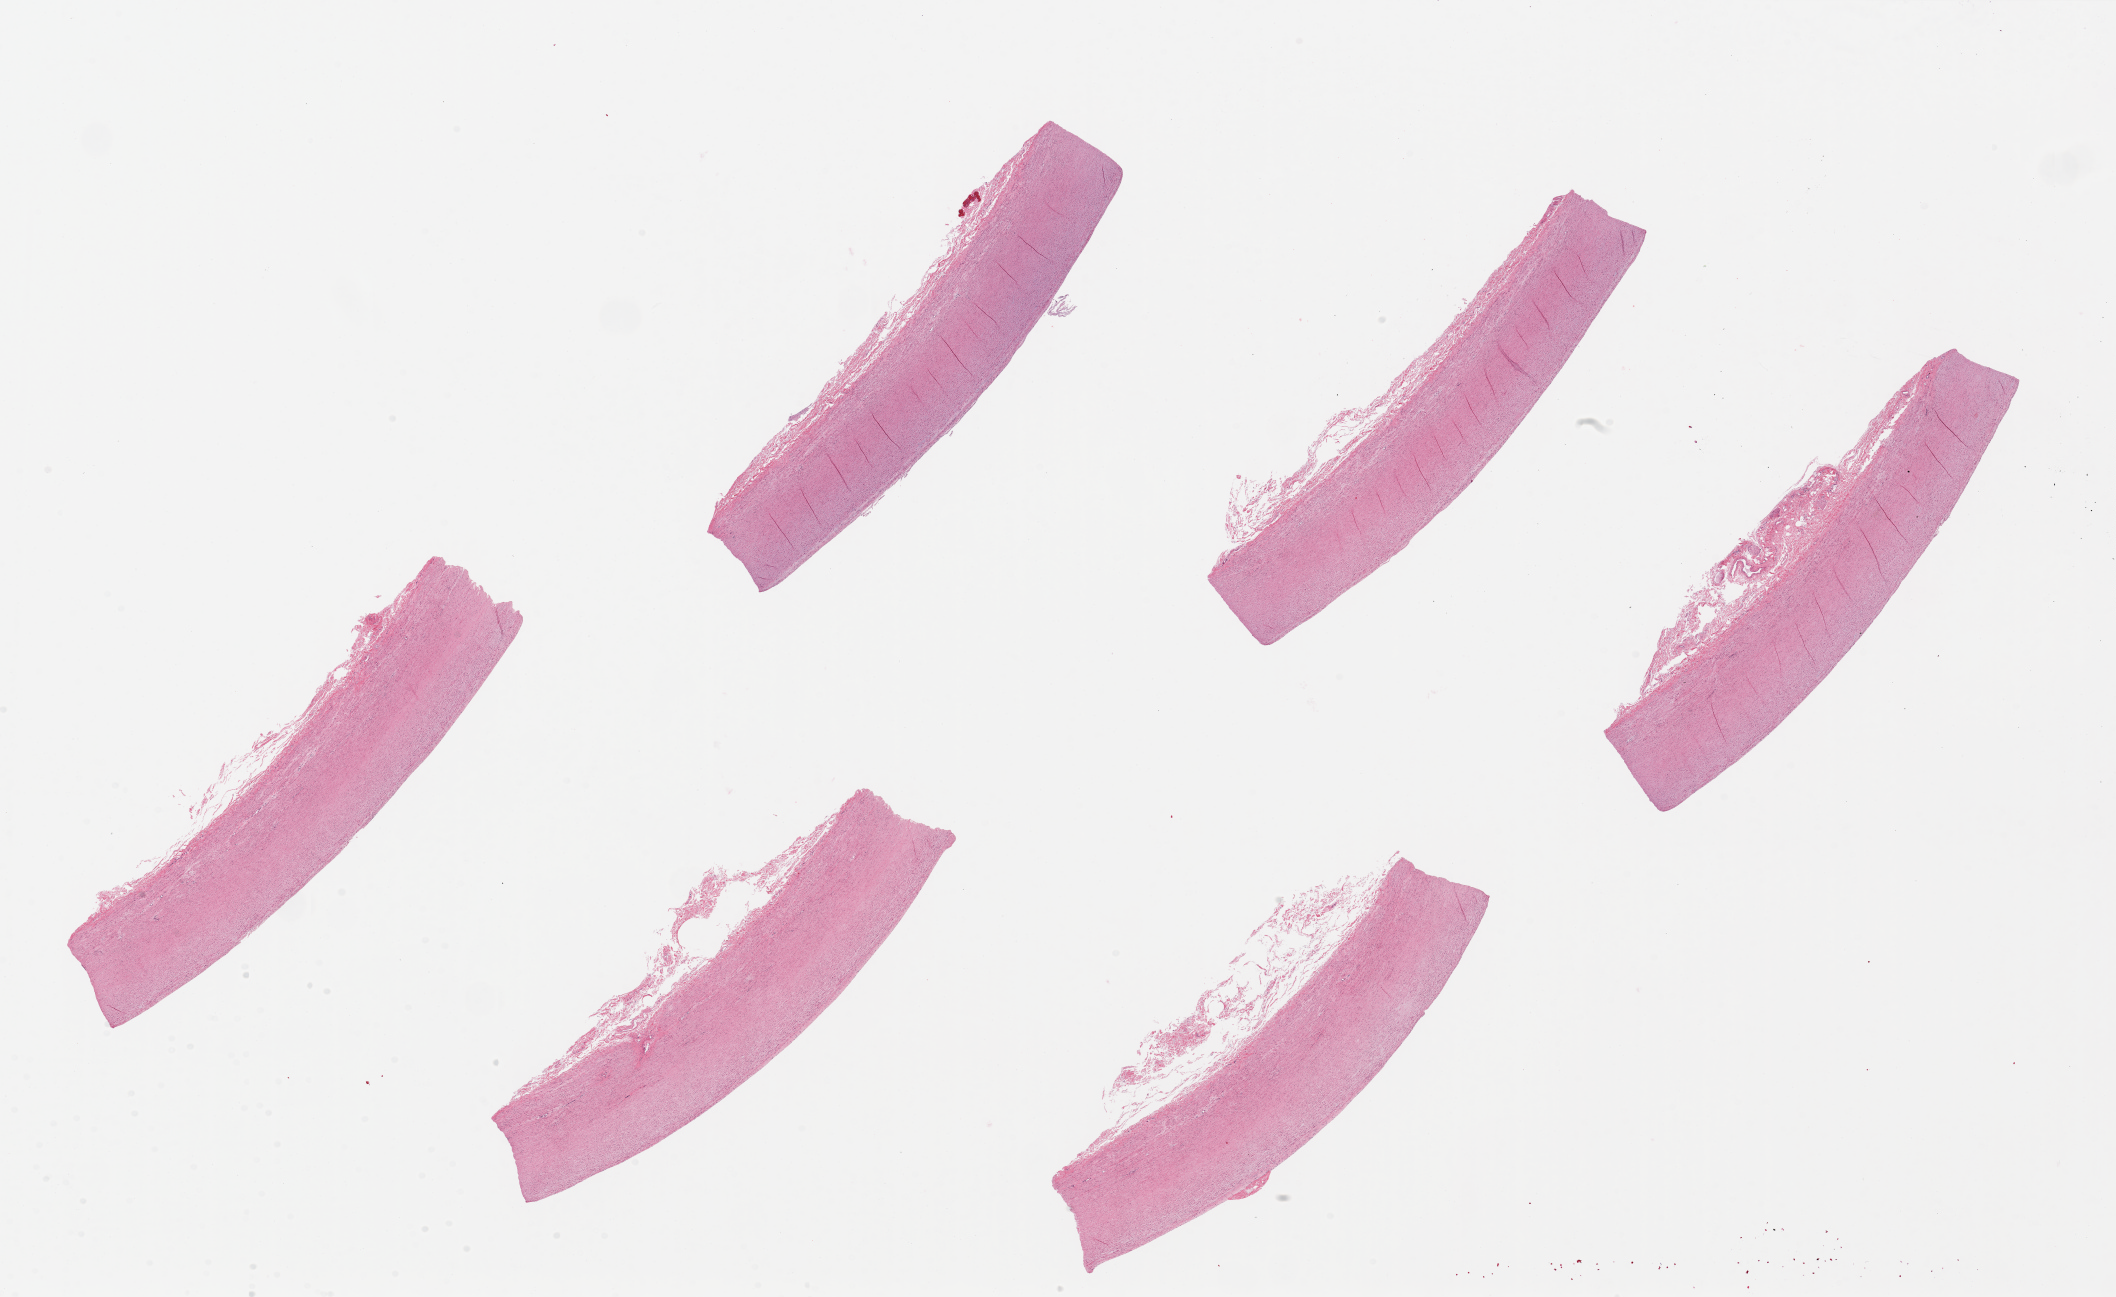
Digitized hematoxylin and eosin (H&E)-stained section, shown as a low-resolution overview of the whole scanned area (about 33.5 x 20.5 mm, slide scanned at 20x); PAXgene-fixed paraffin-embedded (PFPE) section; section of aorta (target tissue); tissue donor sample.
Pathologist's review note for this sample: 6 pieces, up to 9x2mm; no sclerosis; minimal extraneous adventitial tissue.